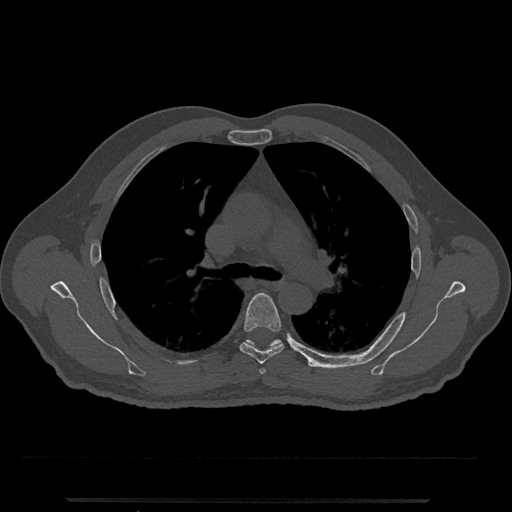
CT including the spine, one axial slice; position 783 of 797 along the scan axis; bone window (W 1800 / L 400 HU); 512 × 512 image matrix, field of view 419 × 419 mm. Patient: male, 63 years. From the clinical record (not read from this slice): primary cancer: prostate.
Outlined on this slice (semi-automatically segmented with operator editing):
- T5 vertebra: bounding box <239,293,284,364> (left, top, right, bottom; pixels)
- T6 vertebra: <244,339,282,347>